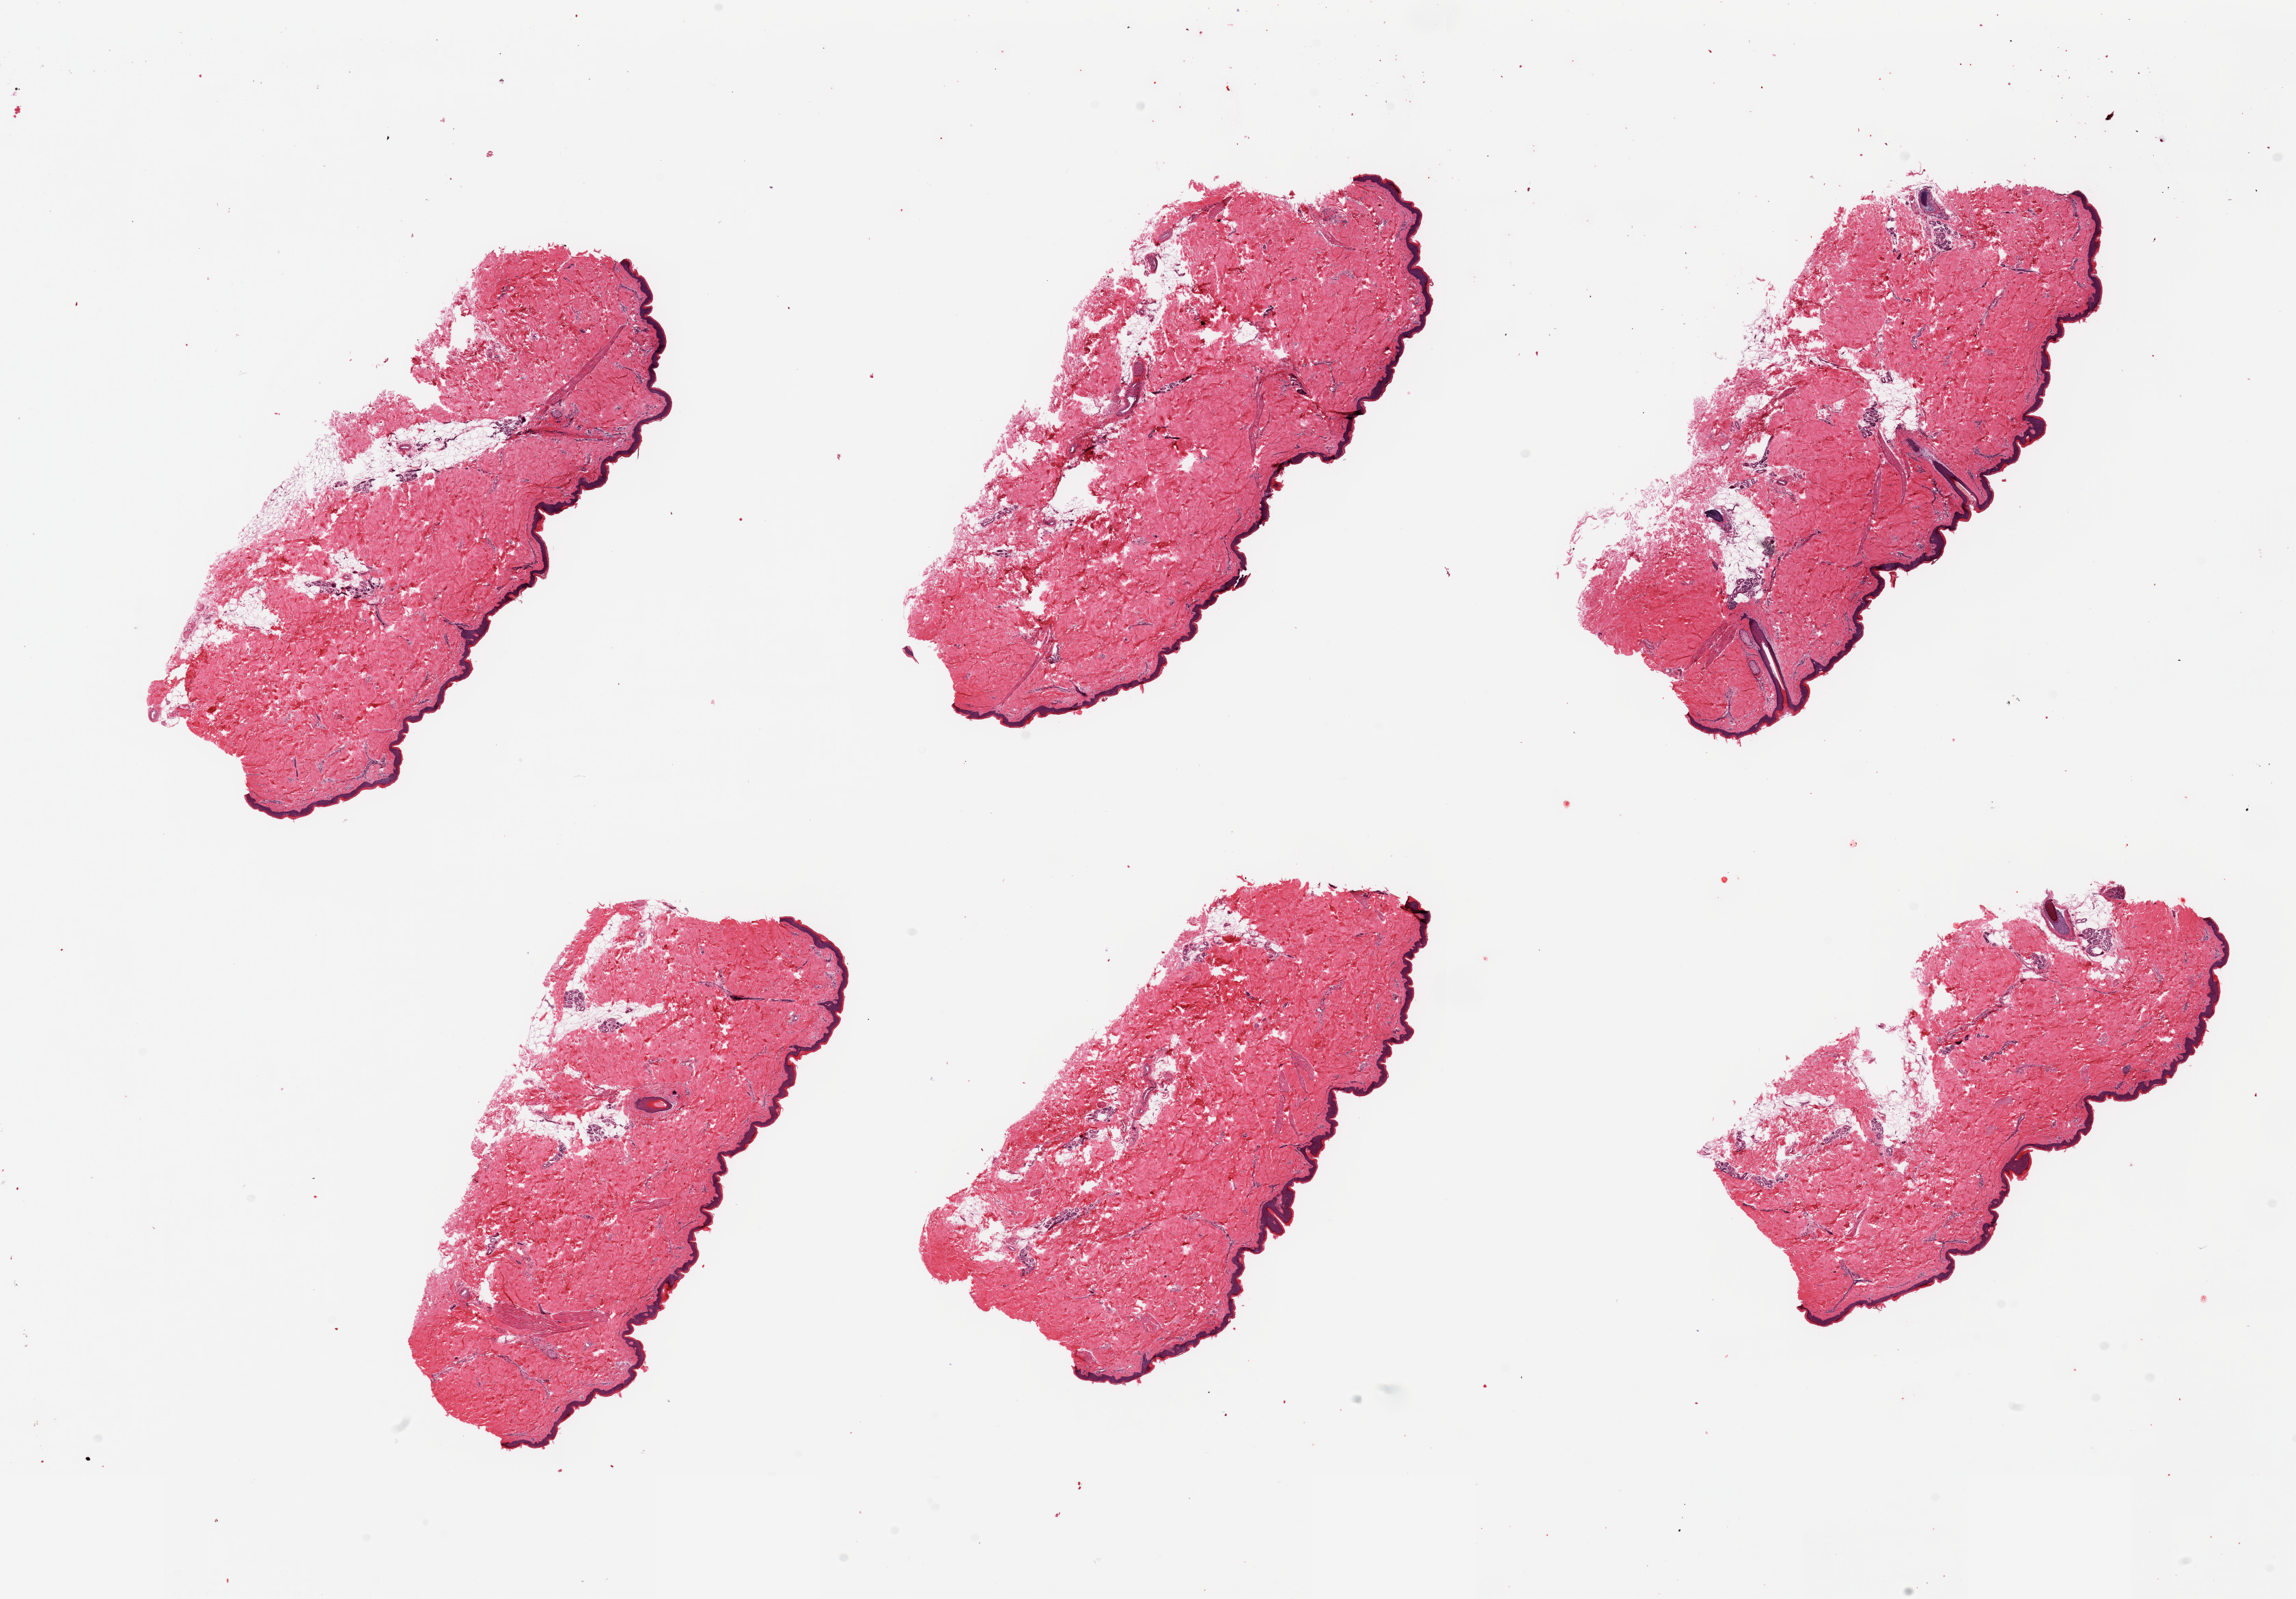
Haematoxylin and eosin whole-slide image — low-resolution overview of the scanned area, about 26.6 x 18.5 mm (acquisition: 20x scan); PAXgene-fixed paraffin-embedded (PFPE) section; section of skin of lower leg (target tissue); tissue donor sample. Donor: male.
Review note (as recorded): 6 pieces; predominantly well trimmed with up to 5-10% internal/external fat. epidermis measures 53 micorns.